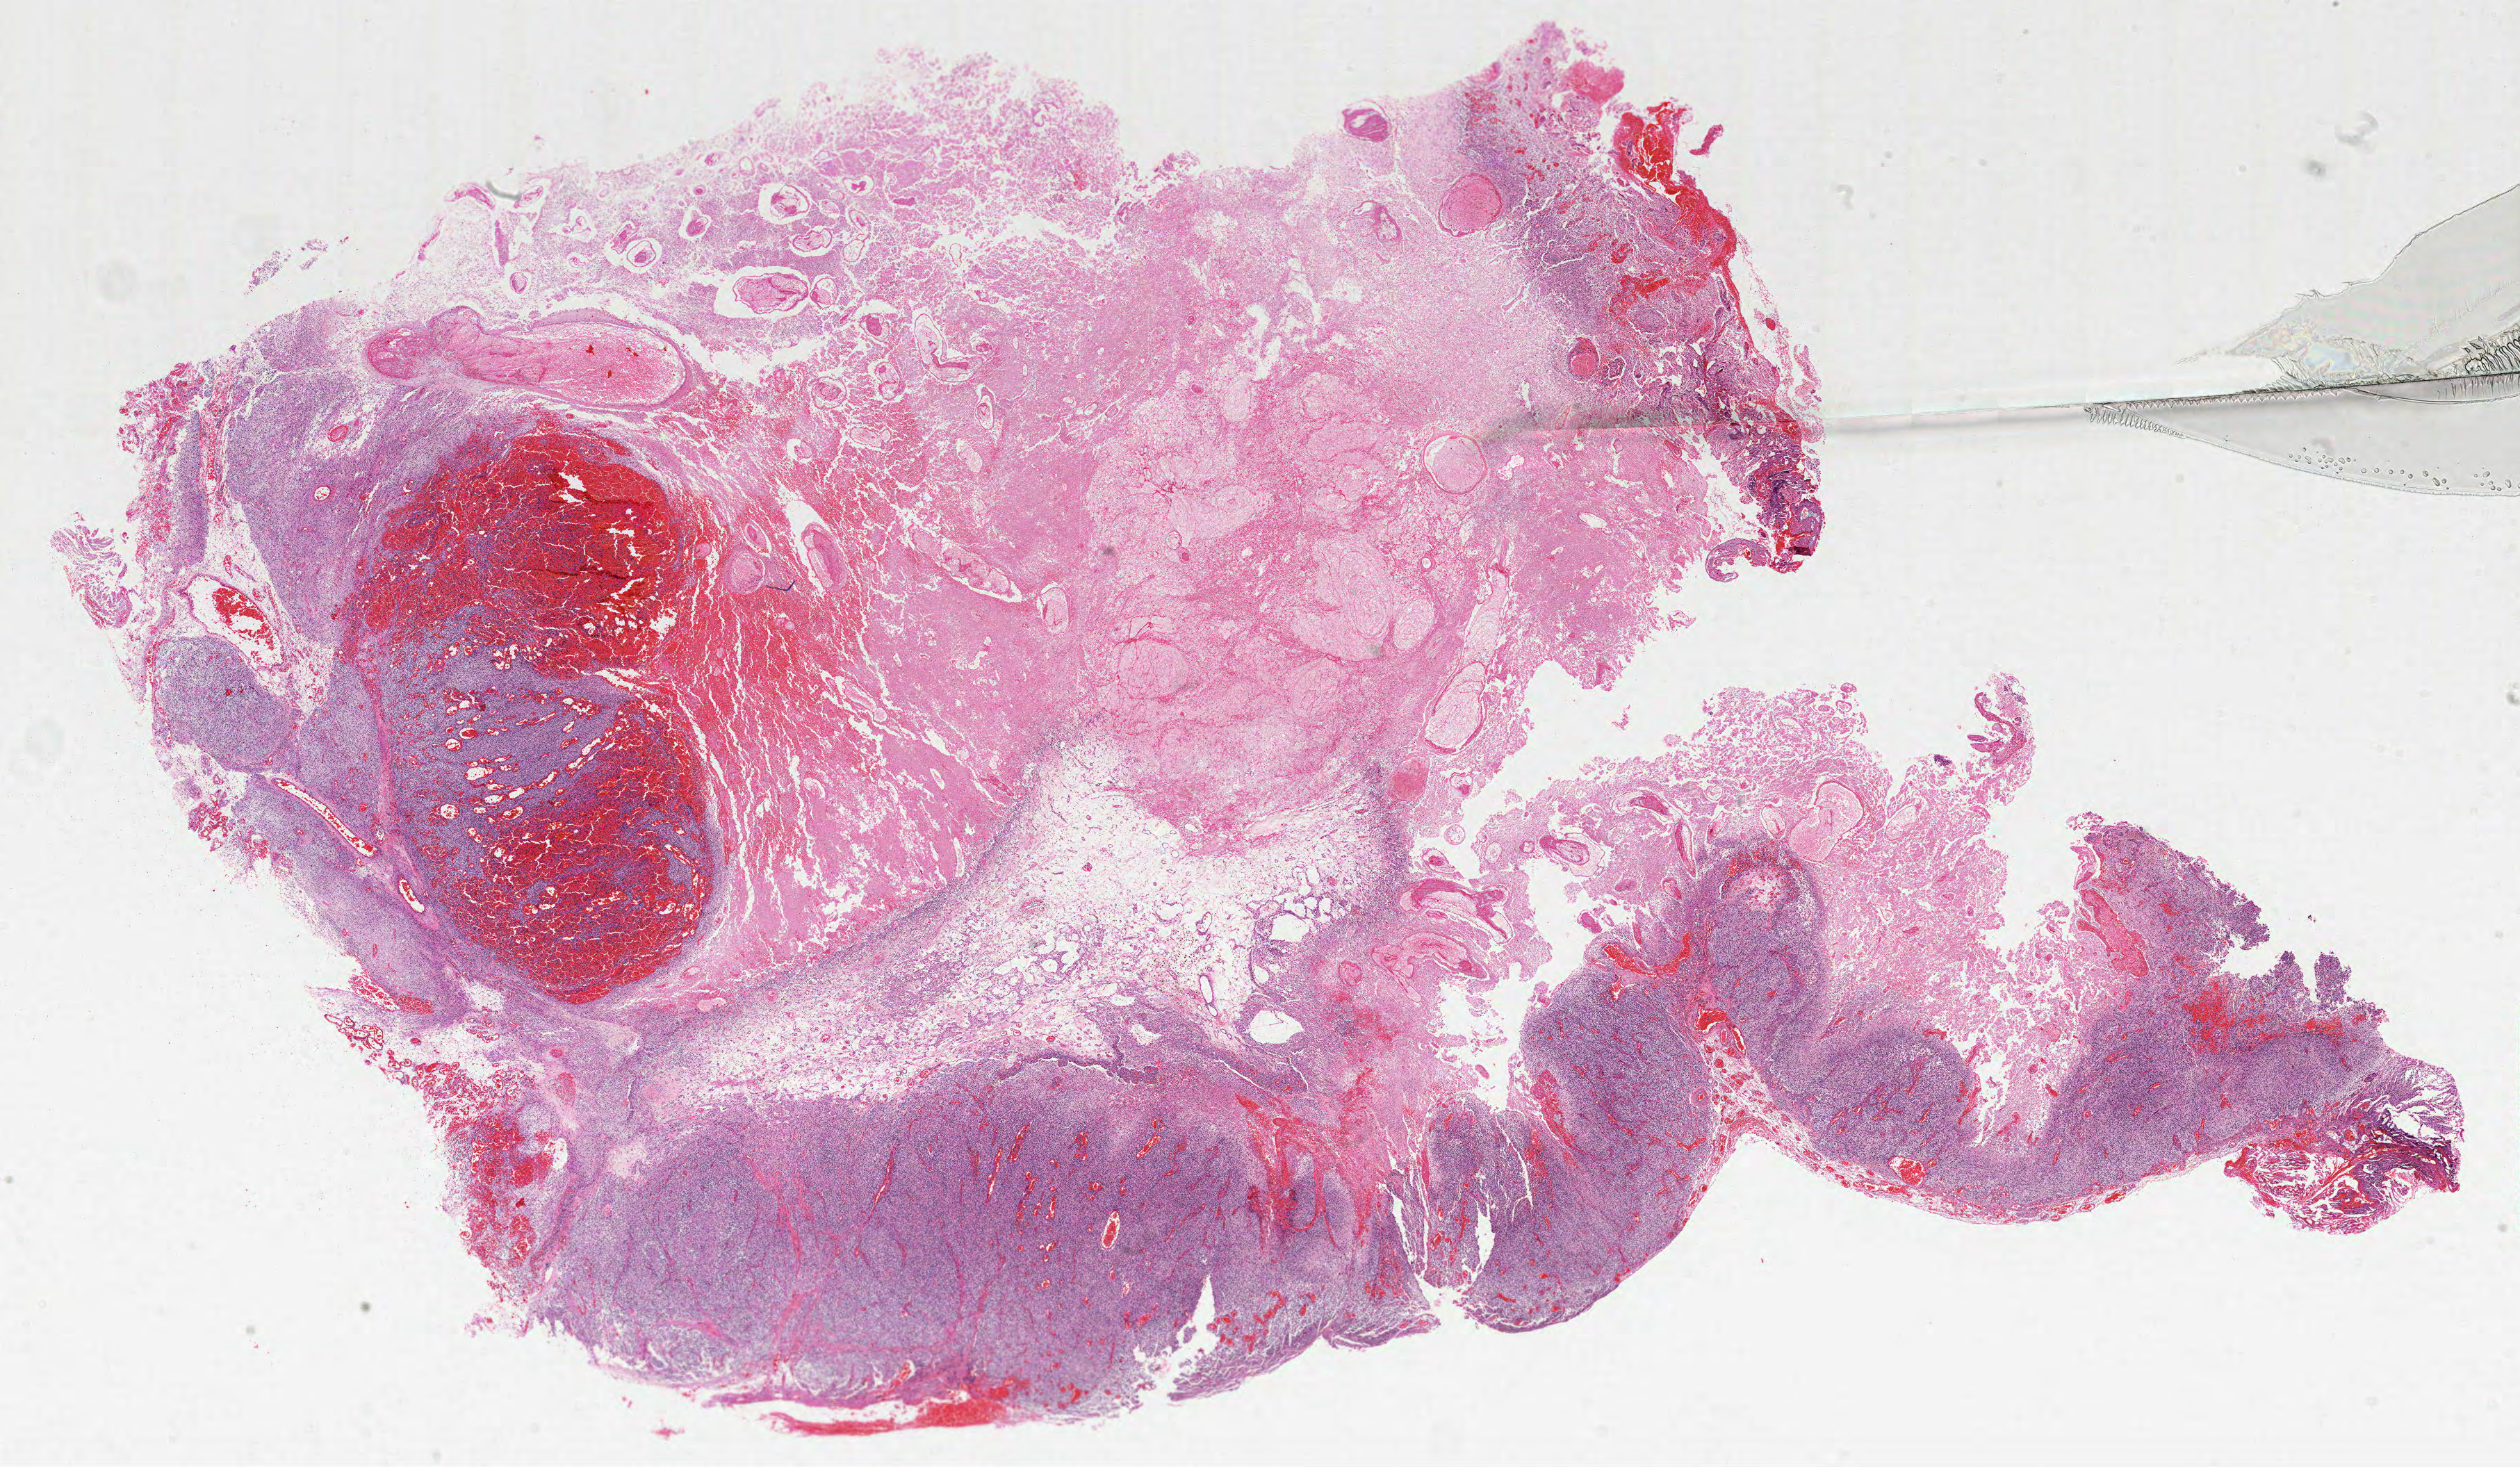
Whole-slide histology image, H&E, a low-resolution overview of the entire scanned area, about 29.0 x 16.9 mm; formalin-fixed paraffin-embedded (FFPE) diagnostic section; brain, primary tumour sample. Male, age 74 years at initial diagnosis.
Histologic diagnosis: Glioblastoma.